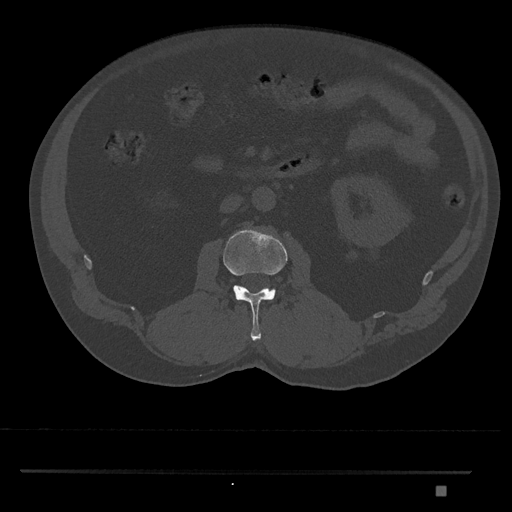
CT including the spine, one axial slice. Position 742 of 1134 along the scan axis. Reconstruction kernel Br40s/3. 120 kVp. Bone window (W 1800 / L 400 HU). 0.5 mm slice thickness. 512 × 512 image matrix, field of view 429 × 429 mm. Male patient, age 65 years. From the clinical record (not read from this slice): primary cancer: prostate.
Outlined on this slice (semi-automatically segmented with operator editing):
- L2 vertebra: box from (x=223, y=228) to (x=288, y=341) px